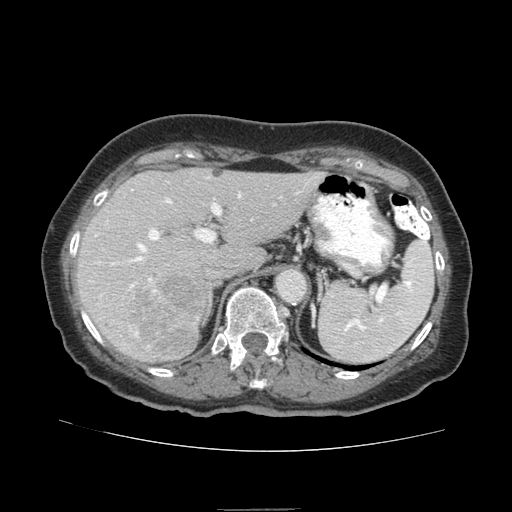
Contrast-enhanced abdominal CT (liver protocol), one axial slice. Position 52 of 95 along the scan axis. Reconstruction kernel STANDARD. 140 kVp. Soft-tissue window (W 400 / L 40 HU). 2.5 mm slice thickness. 512 × 512 image matrix, field of view 360 × 360 mm. Case-level facts recorded for this patient, not image findings: diagnosis: hepatocellular carcinoma (patient treated with transarterial chemoembolisation; whether this scan precedes or follows treatment is not stated here); TNM stage (as recorded): Stage-IVA; Child-Pugh class: B; tumour differentiation: moderately differentiated.
Outlined on this slice (semi-automatically segmented with operator editing):
- liver parenchyma outside the tumour (the mass and vessels are separate outlines, so this box may not span the whole liver): bounding box <76,168,324,362> (left, top, right, bottom; pixels)
- mass: <130,273,207,355>
- liver vessels: <111,192,299,289>